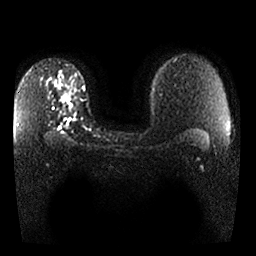
Breast MRI, one axial slice. Slice 18 of 25 in the series (ordered by position). Diffusion-weighted series; image 2 of 4 stored at this slice position (different b-values; order by instance number). 1.5 T. 4 mm slice thickness. 256 × 256 image matrix. Female patient.
Outlined on this slice (expert manual segmentation):
- tumour on diffusion-weighted imaging: bounding box (x1, y1, x2, y2) in pixels: (58, 94, 71, 104)